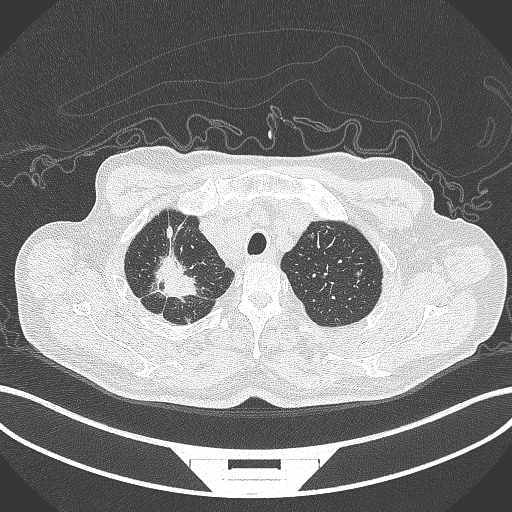
Chest CT, one axial slice; slice 334 of 407 in the series (ordered by position); reconstruction kernel B70f; lung window (W 1500 / L -600 HU); 1 mm slice thickness; 512 × 512 image matrix. Male patient, age 69 years. Case-level facts recorded for this patient, not image findings: clinical TNM (as recorded): T1c N1 M1.
Structures marked on this image (bounding box drawn by a radiologist):
- lung tumour (recorded histology: adenocarcinoma): bounding box <148,246,208,300> (left, top, right, bottom; pixels)